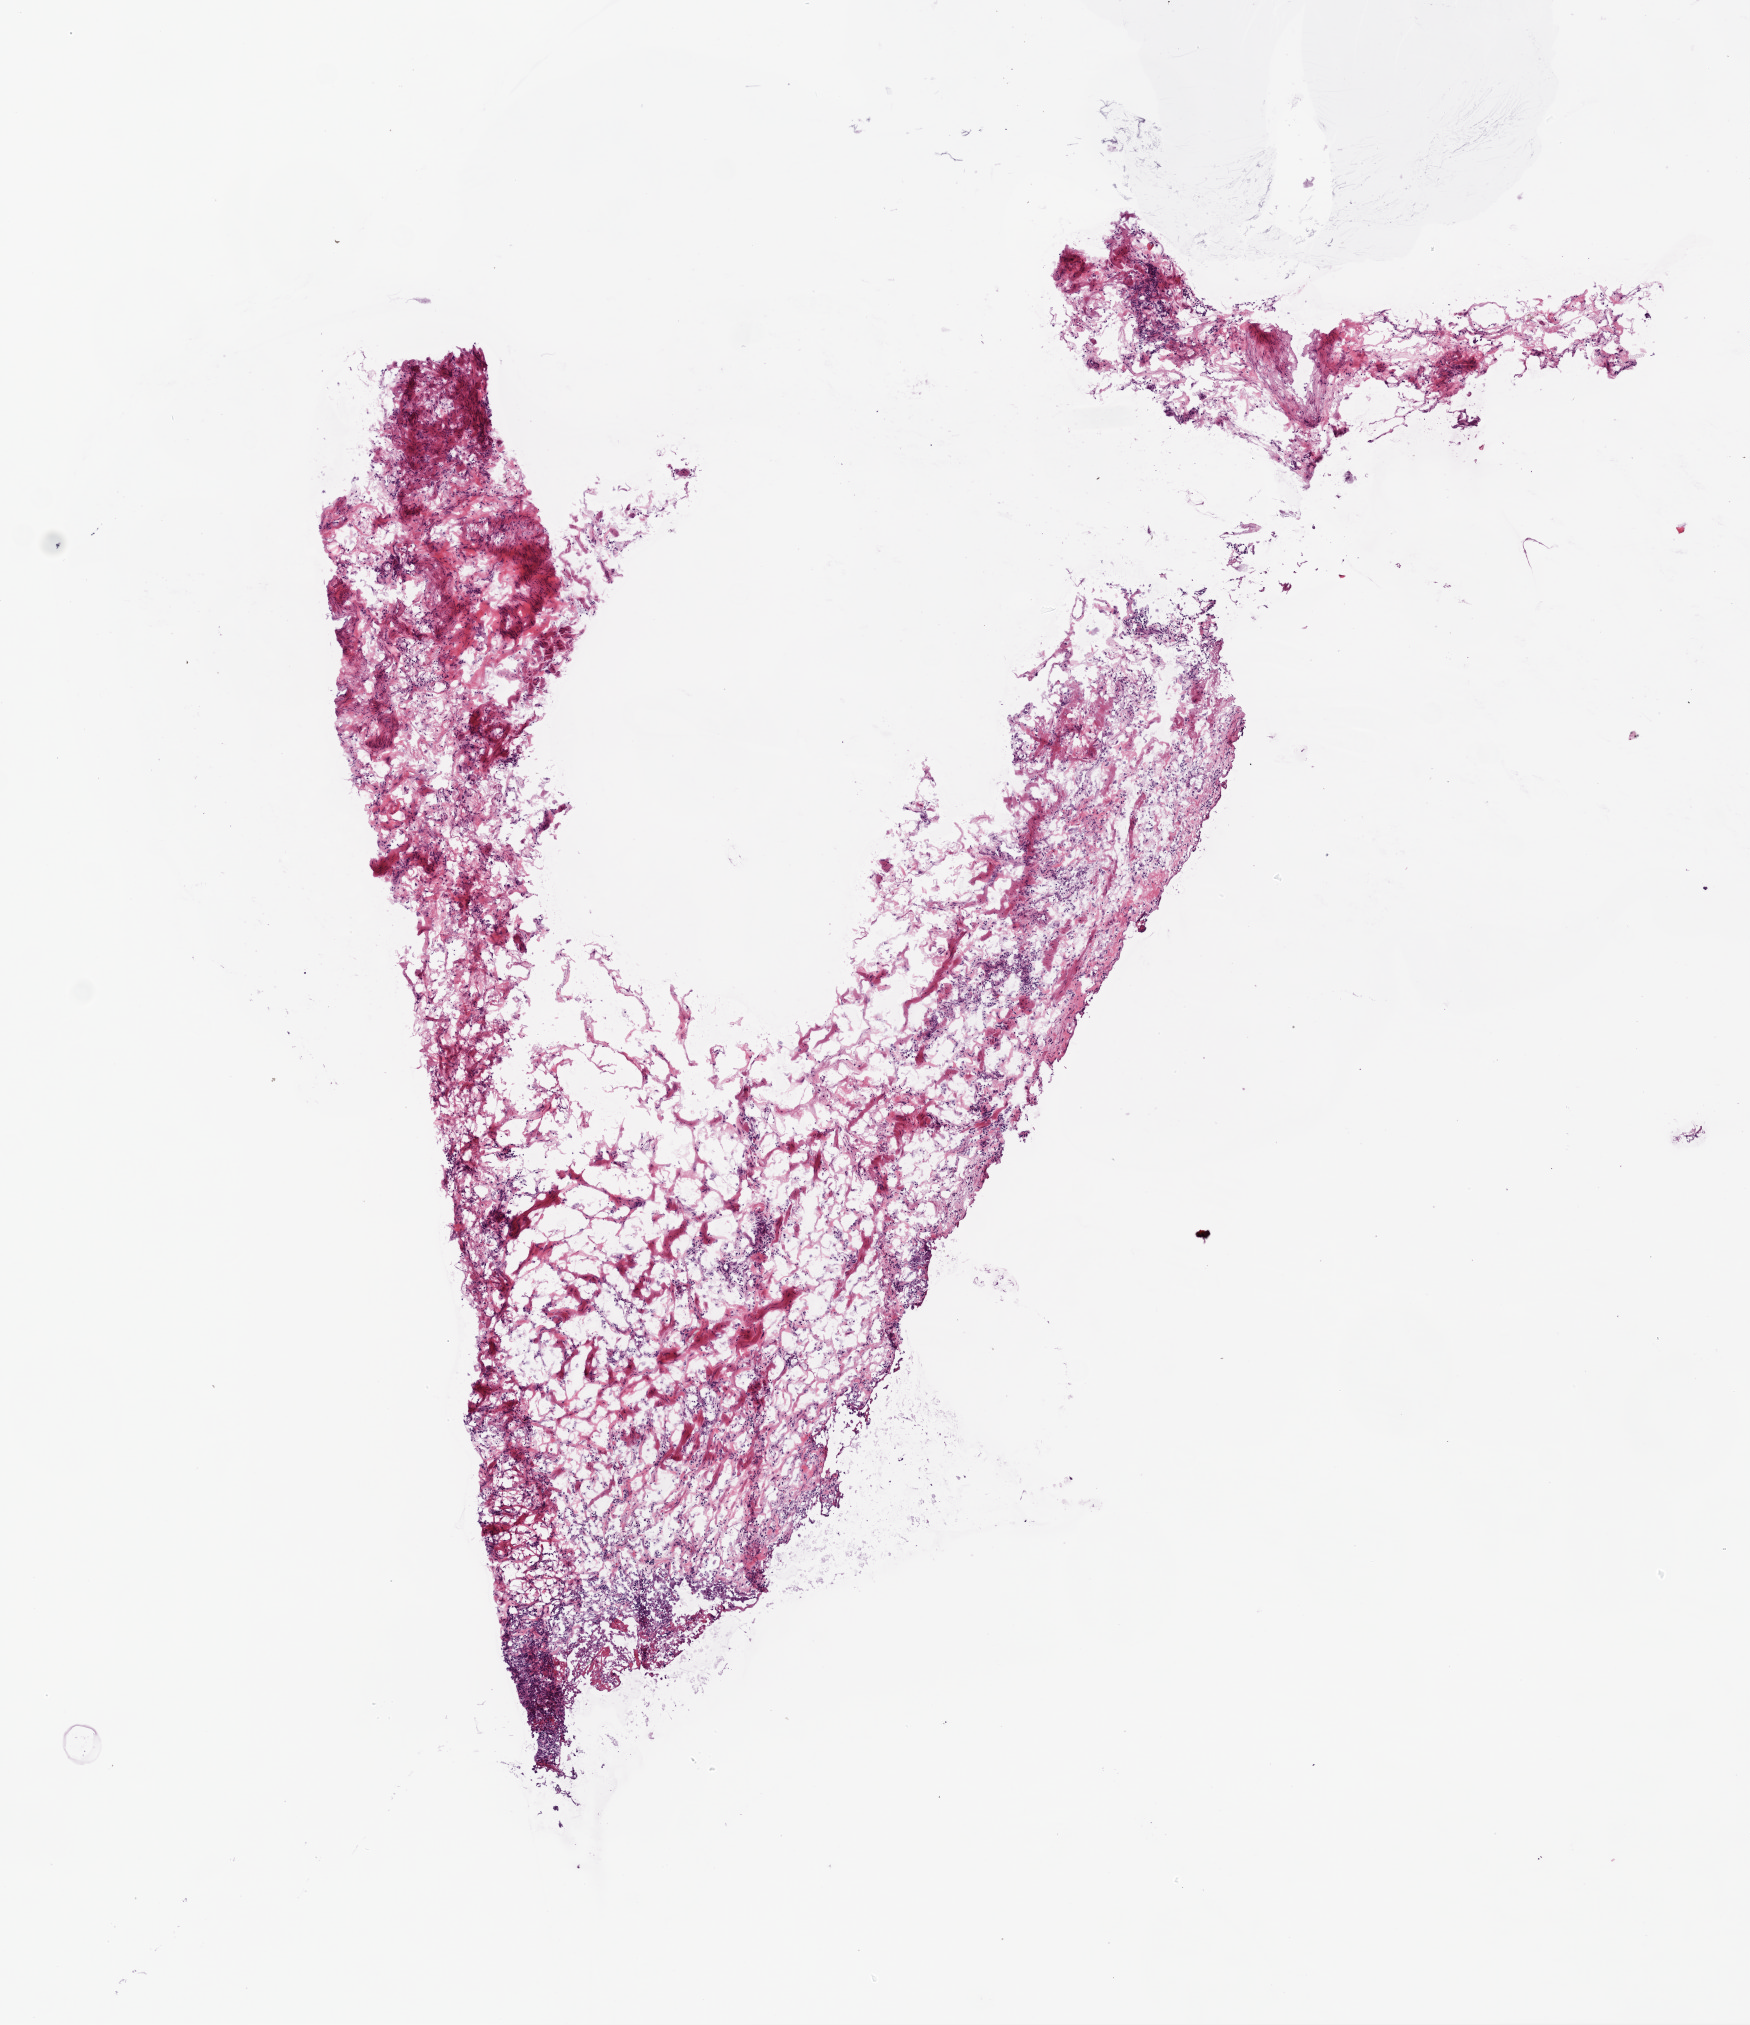
Digitized H&E tissue section (whole slide), low-resolution overview of the scanned area, about 7.0 x 8.1 mm. Frozen section from the bottom of the tissue portion. Ovary, solid tissue normal (non-tumour tissue) sample. Patient: female, age at initial diagnosis 65 years.
- this section: solid tissue normal (non-tumour) sample from the same patient
- patient diagnosis: Serous cystadenocarcinoma, NOS